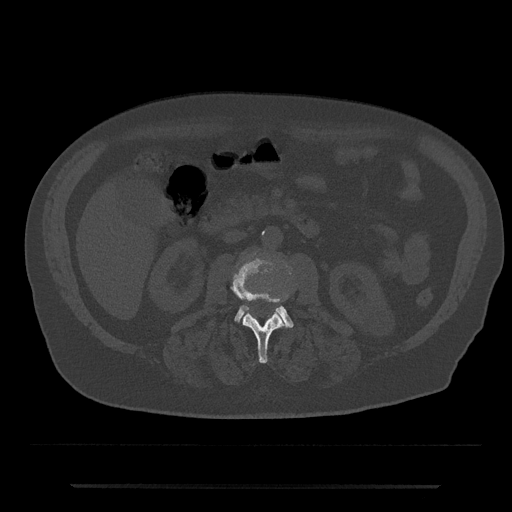
CT including the spine, one axial slice; position 448 of 797 along the scan axis; reconstruction kernel Br40s/3; 120 kVp; bone window (W 1800 / L 400 HU); 0.5 mm slice thickness; 512 × 512 image matrix. Male patient, age 80 years. From the clinical record (not read from this slice): primary cancer: prostate.
Structures marked on this image (semi-automatic segmentation, software-assisted and operator-edited):
- L2 vertebra: bounding box [x1, y1, x2, y2] px = [232, 259, 287, 363]
- L3 vertebra: [234, 305, 294, 328]